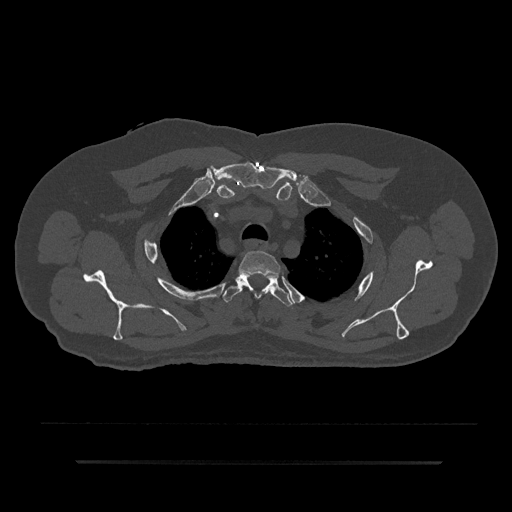
CT including the spine, one axial slice; position 675 of 797 along the scan axis; reconstruction kernel Br40s/3; bone window (W 1800 / L 400 HU); 0.5 mm slice thickness; 512 × 512 image matrix, field of view 464 × 464 mm. Patient: male, 59 years. Case-level facts recorded for this patient, not image findings: primary cancer: bile ducts; vertebrae with lytic lesions (as recorded): T10.
Structures marked on this image (semi-automatic segmentation, software-assisted and operator-edited):
- T2 vertebra: box from (x=238, y=251) to (x=281, y=277) px
- T3 vertebra: (x=222, y=273)–(x=293, y=306)